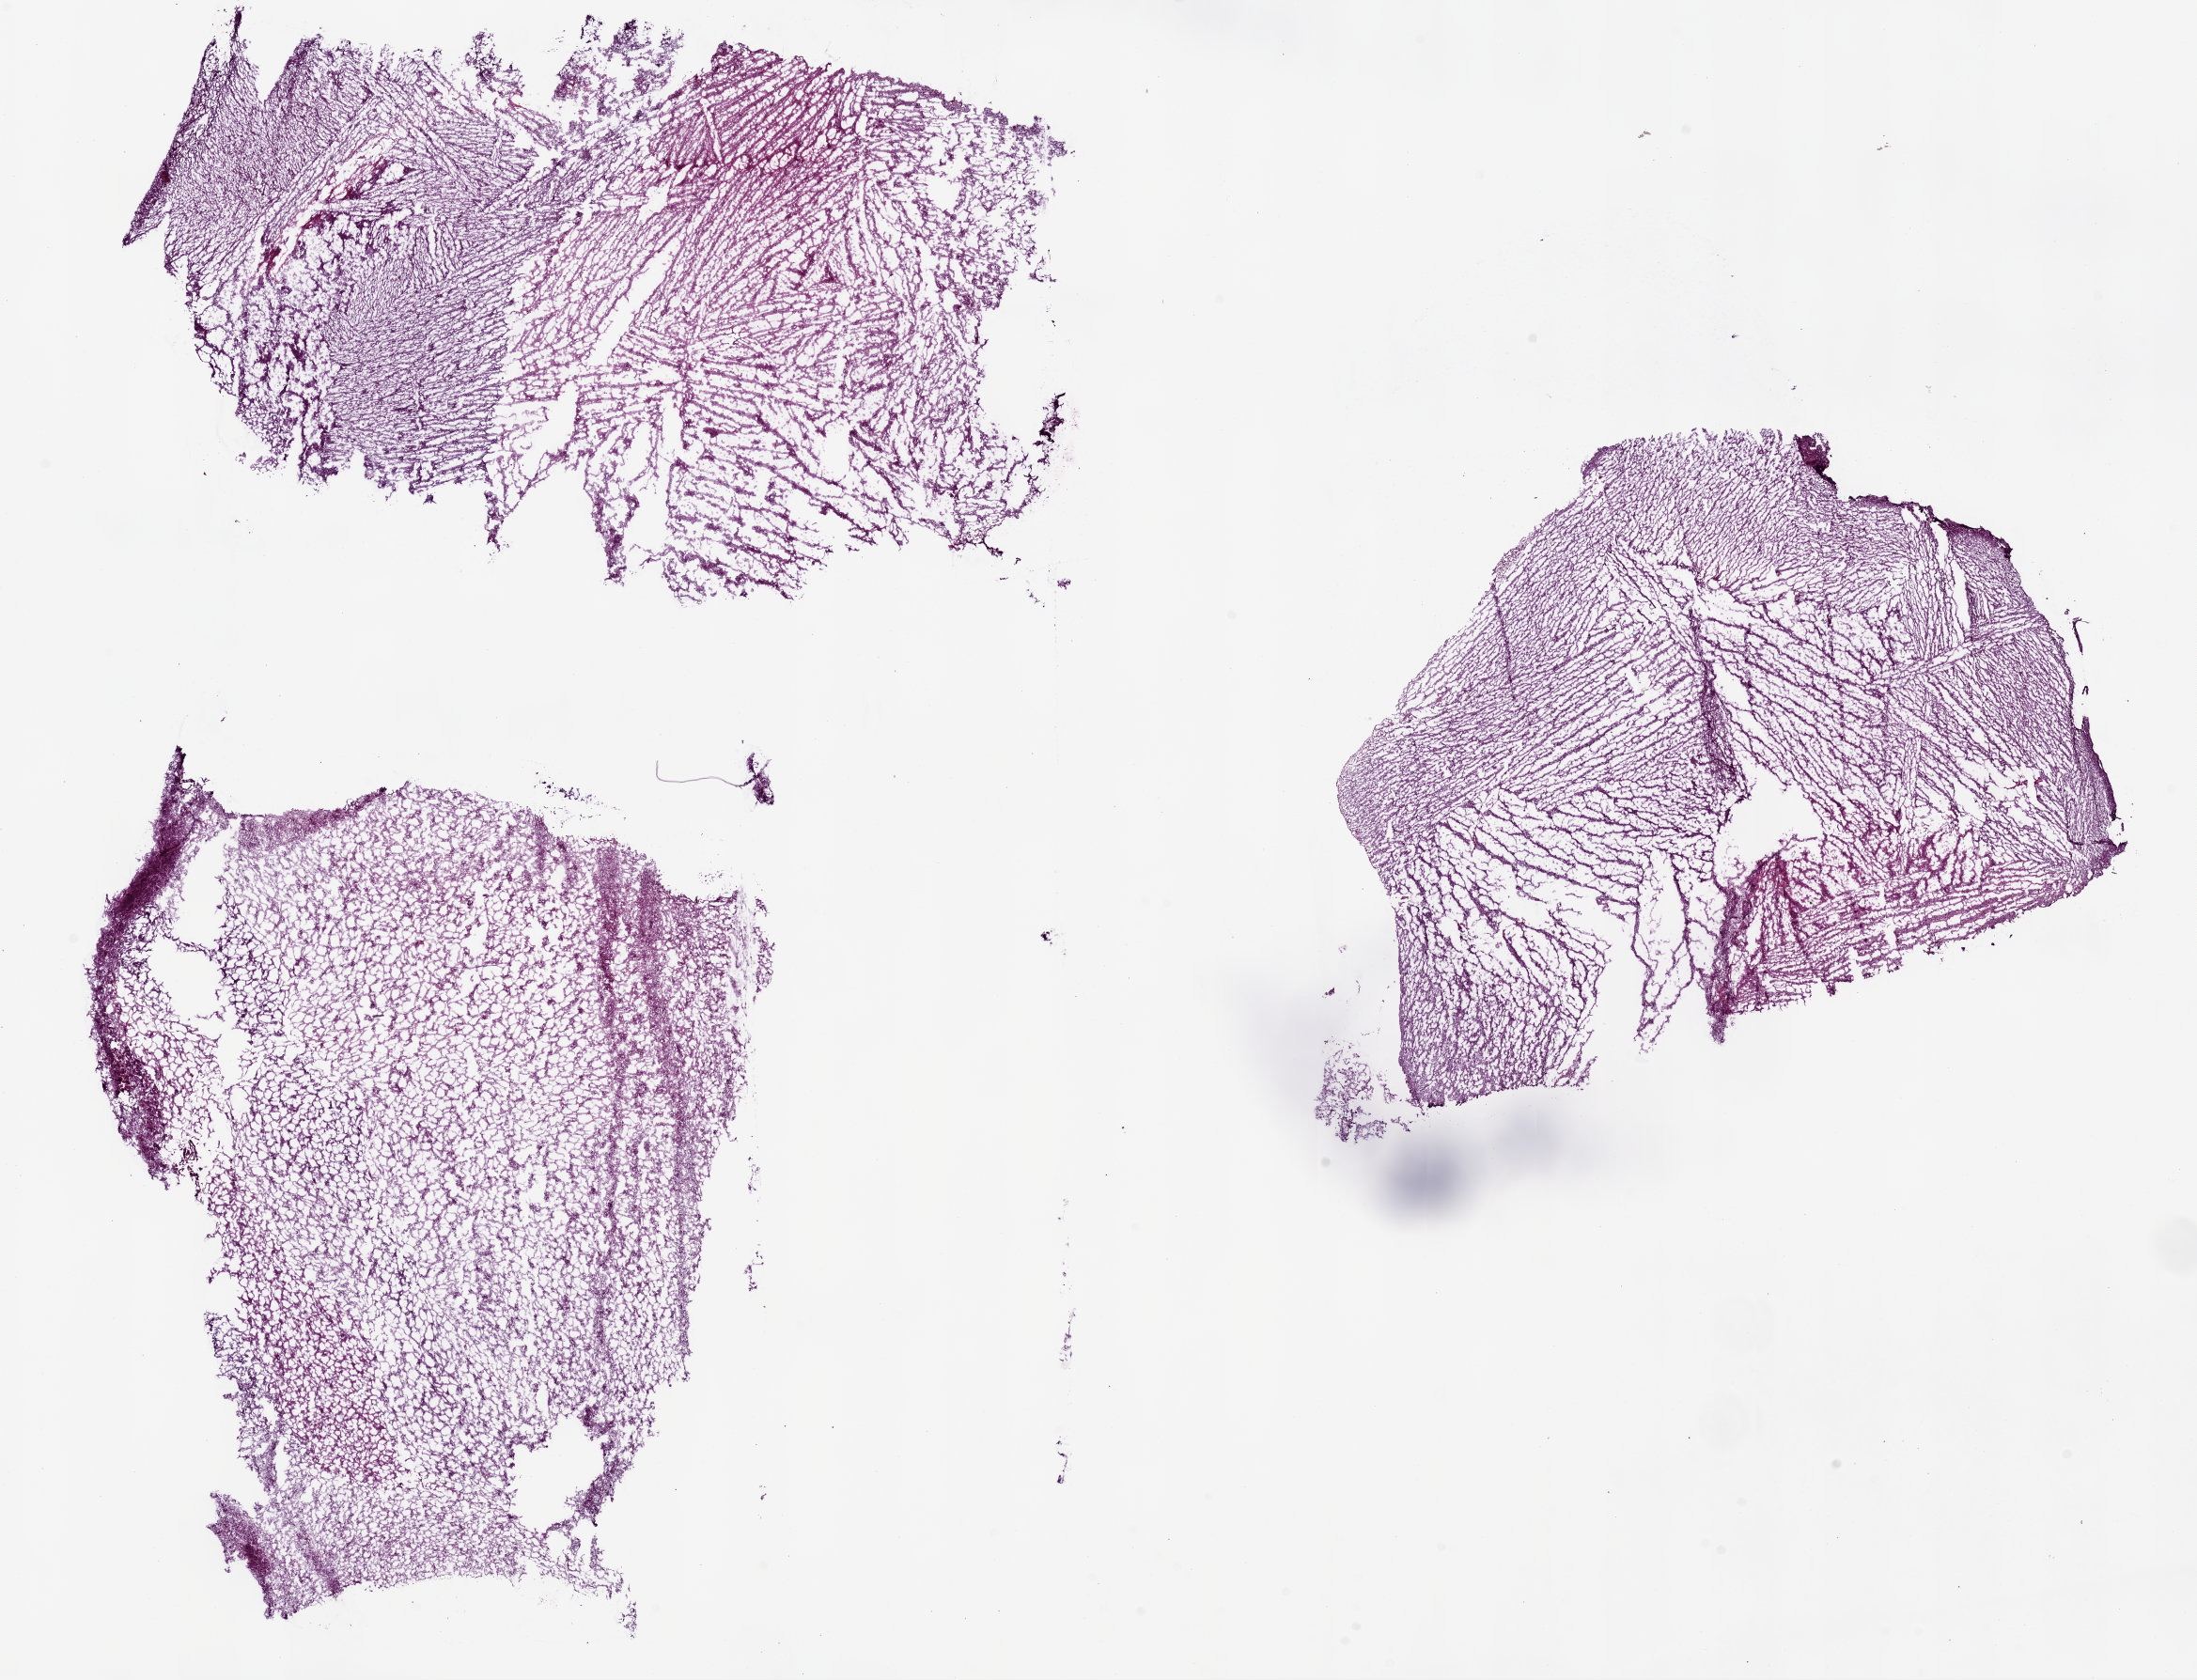
H&E whole-slide image, shown as a low-resolution overview of the whole scanned area (about 18.7 x 14.3 mm). Frozen section. Brain, primary tumour sample. Male patient; age at initial diagnosis 39 years. Histologic grade: G3 (poorly differentiated). Slide review estimates, as recorded: tumour cells 100%, tumour nuclei 75%, normal cells 0%, stromal cells 0%, necrosis 0%.
* pathologic diagnosis: Astrocytoma, anaplastic
* laterality: left